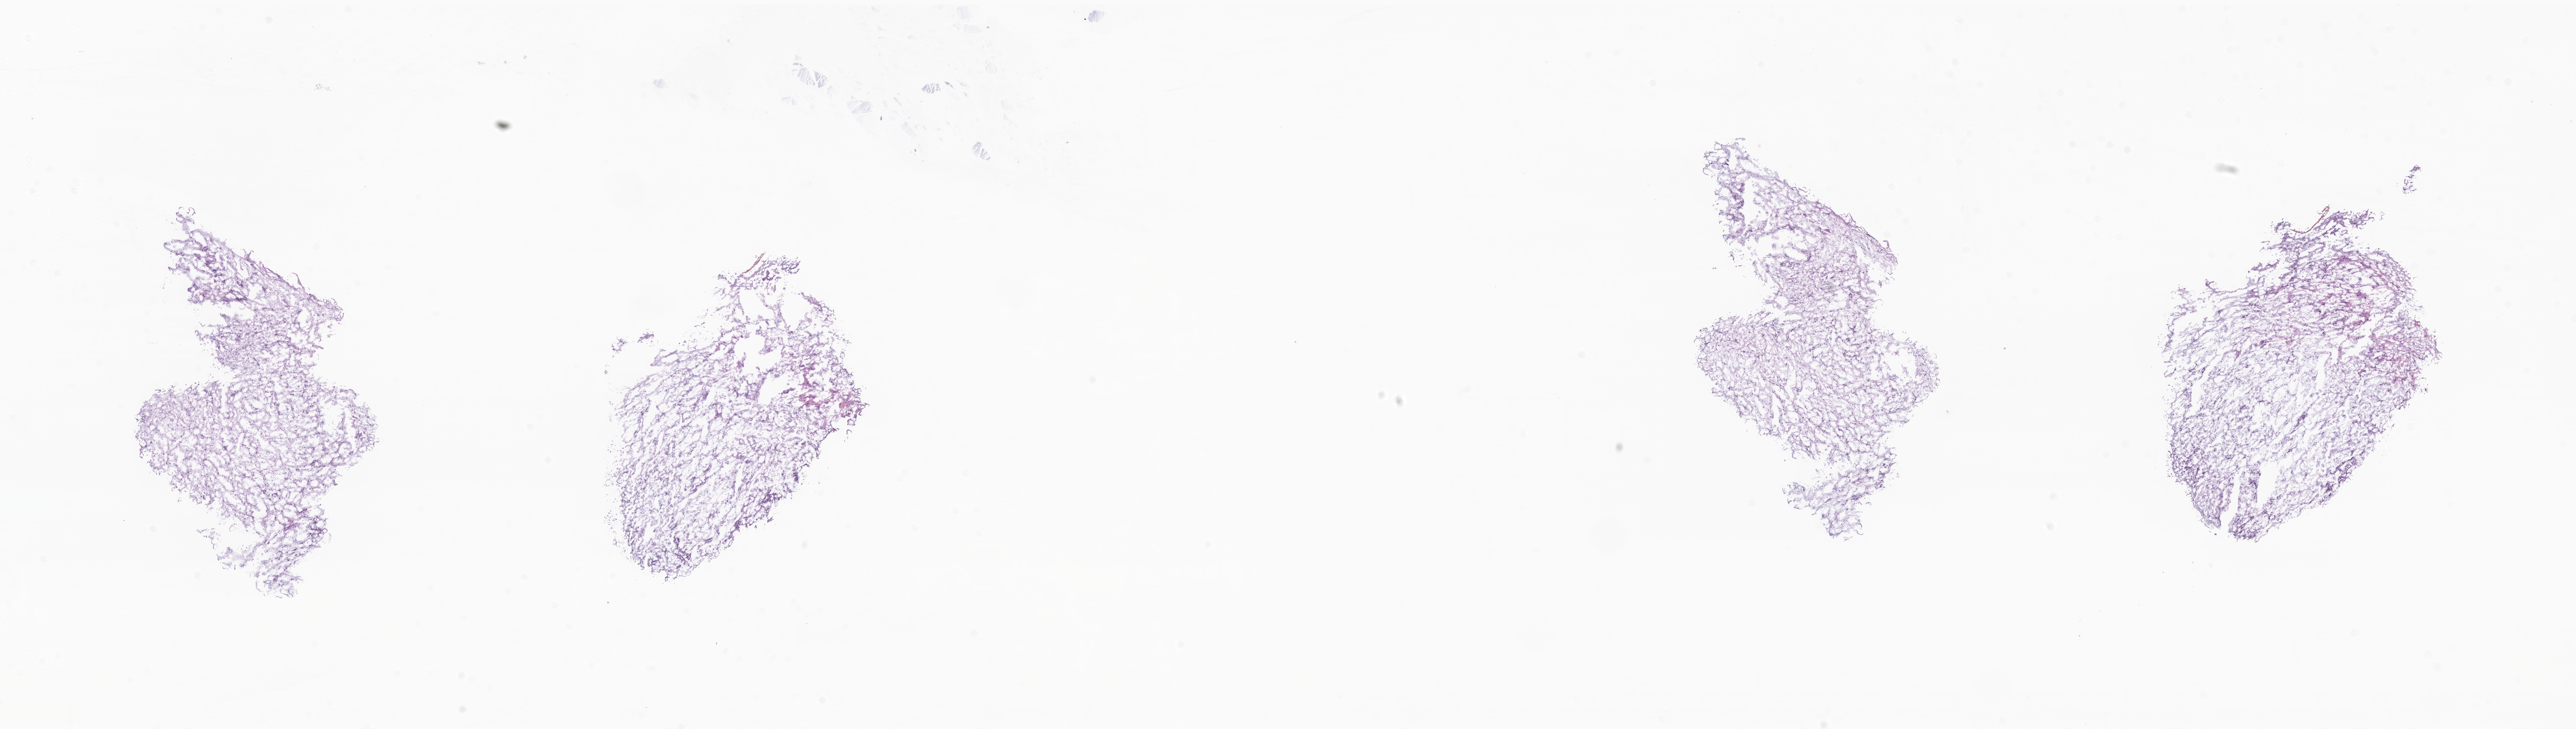
Hematoxylin and eosin (H&E) whole-slide image of tumor tissue from the brain, shown as a low-resolution overview of the whole scanned area (about 35.3 x 10.0 mm), frozen section. Female patient, age 352 days.
Recorded diagnosis: Sarcoma, NOS.